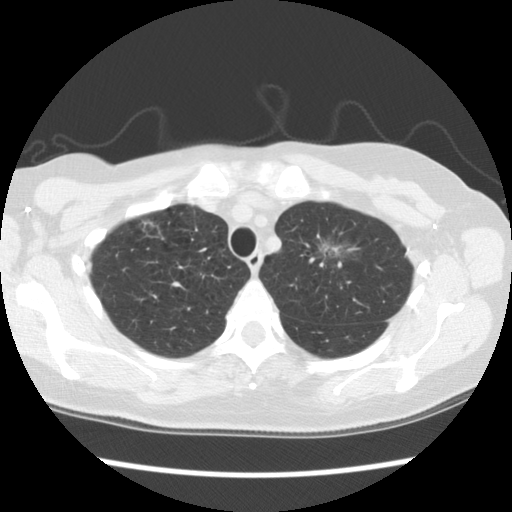
Axial slice from a low-dose chest CT screening exam. Second screening round (one year after baseline). Lung window (W 1500 / L -600 HU). 2.5 mm slice thickness. Slice 86 of 110 in the series. 512 × 512 image matrix. Female participant, aged 65 years at enrolment. Former smoker at enrolment.
Expert-annotated lung lesion, bounding box [x1, y1, x2, y2] px = [300, 224, 364, 284]. The screening reader recorded 2 non-calcified nodules or masses ≥4 mm on this exam (right upper lobe, left upper lobe); which of them this box marks is not recorded. Official screen result: positive, other. Participant outcome: lung cancer diagnosed 481 days after this screen (after the third annual screen) — adenocarcinoma, NOS, left upper lobe, moderately differentiated (G2), stage IA (AJCC 6th edition), 30 mm at pathology.